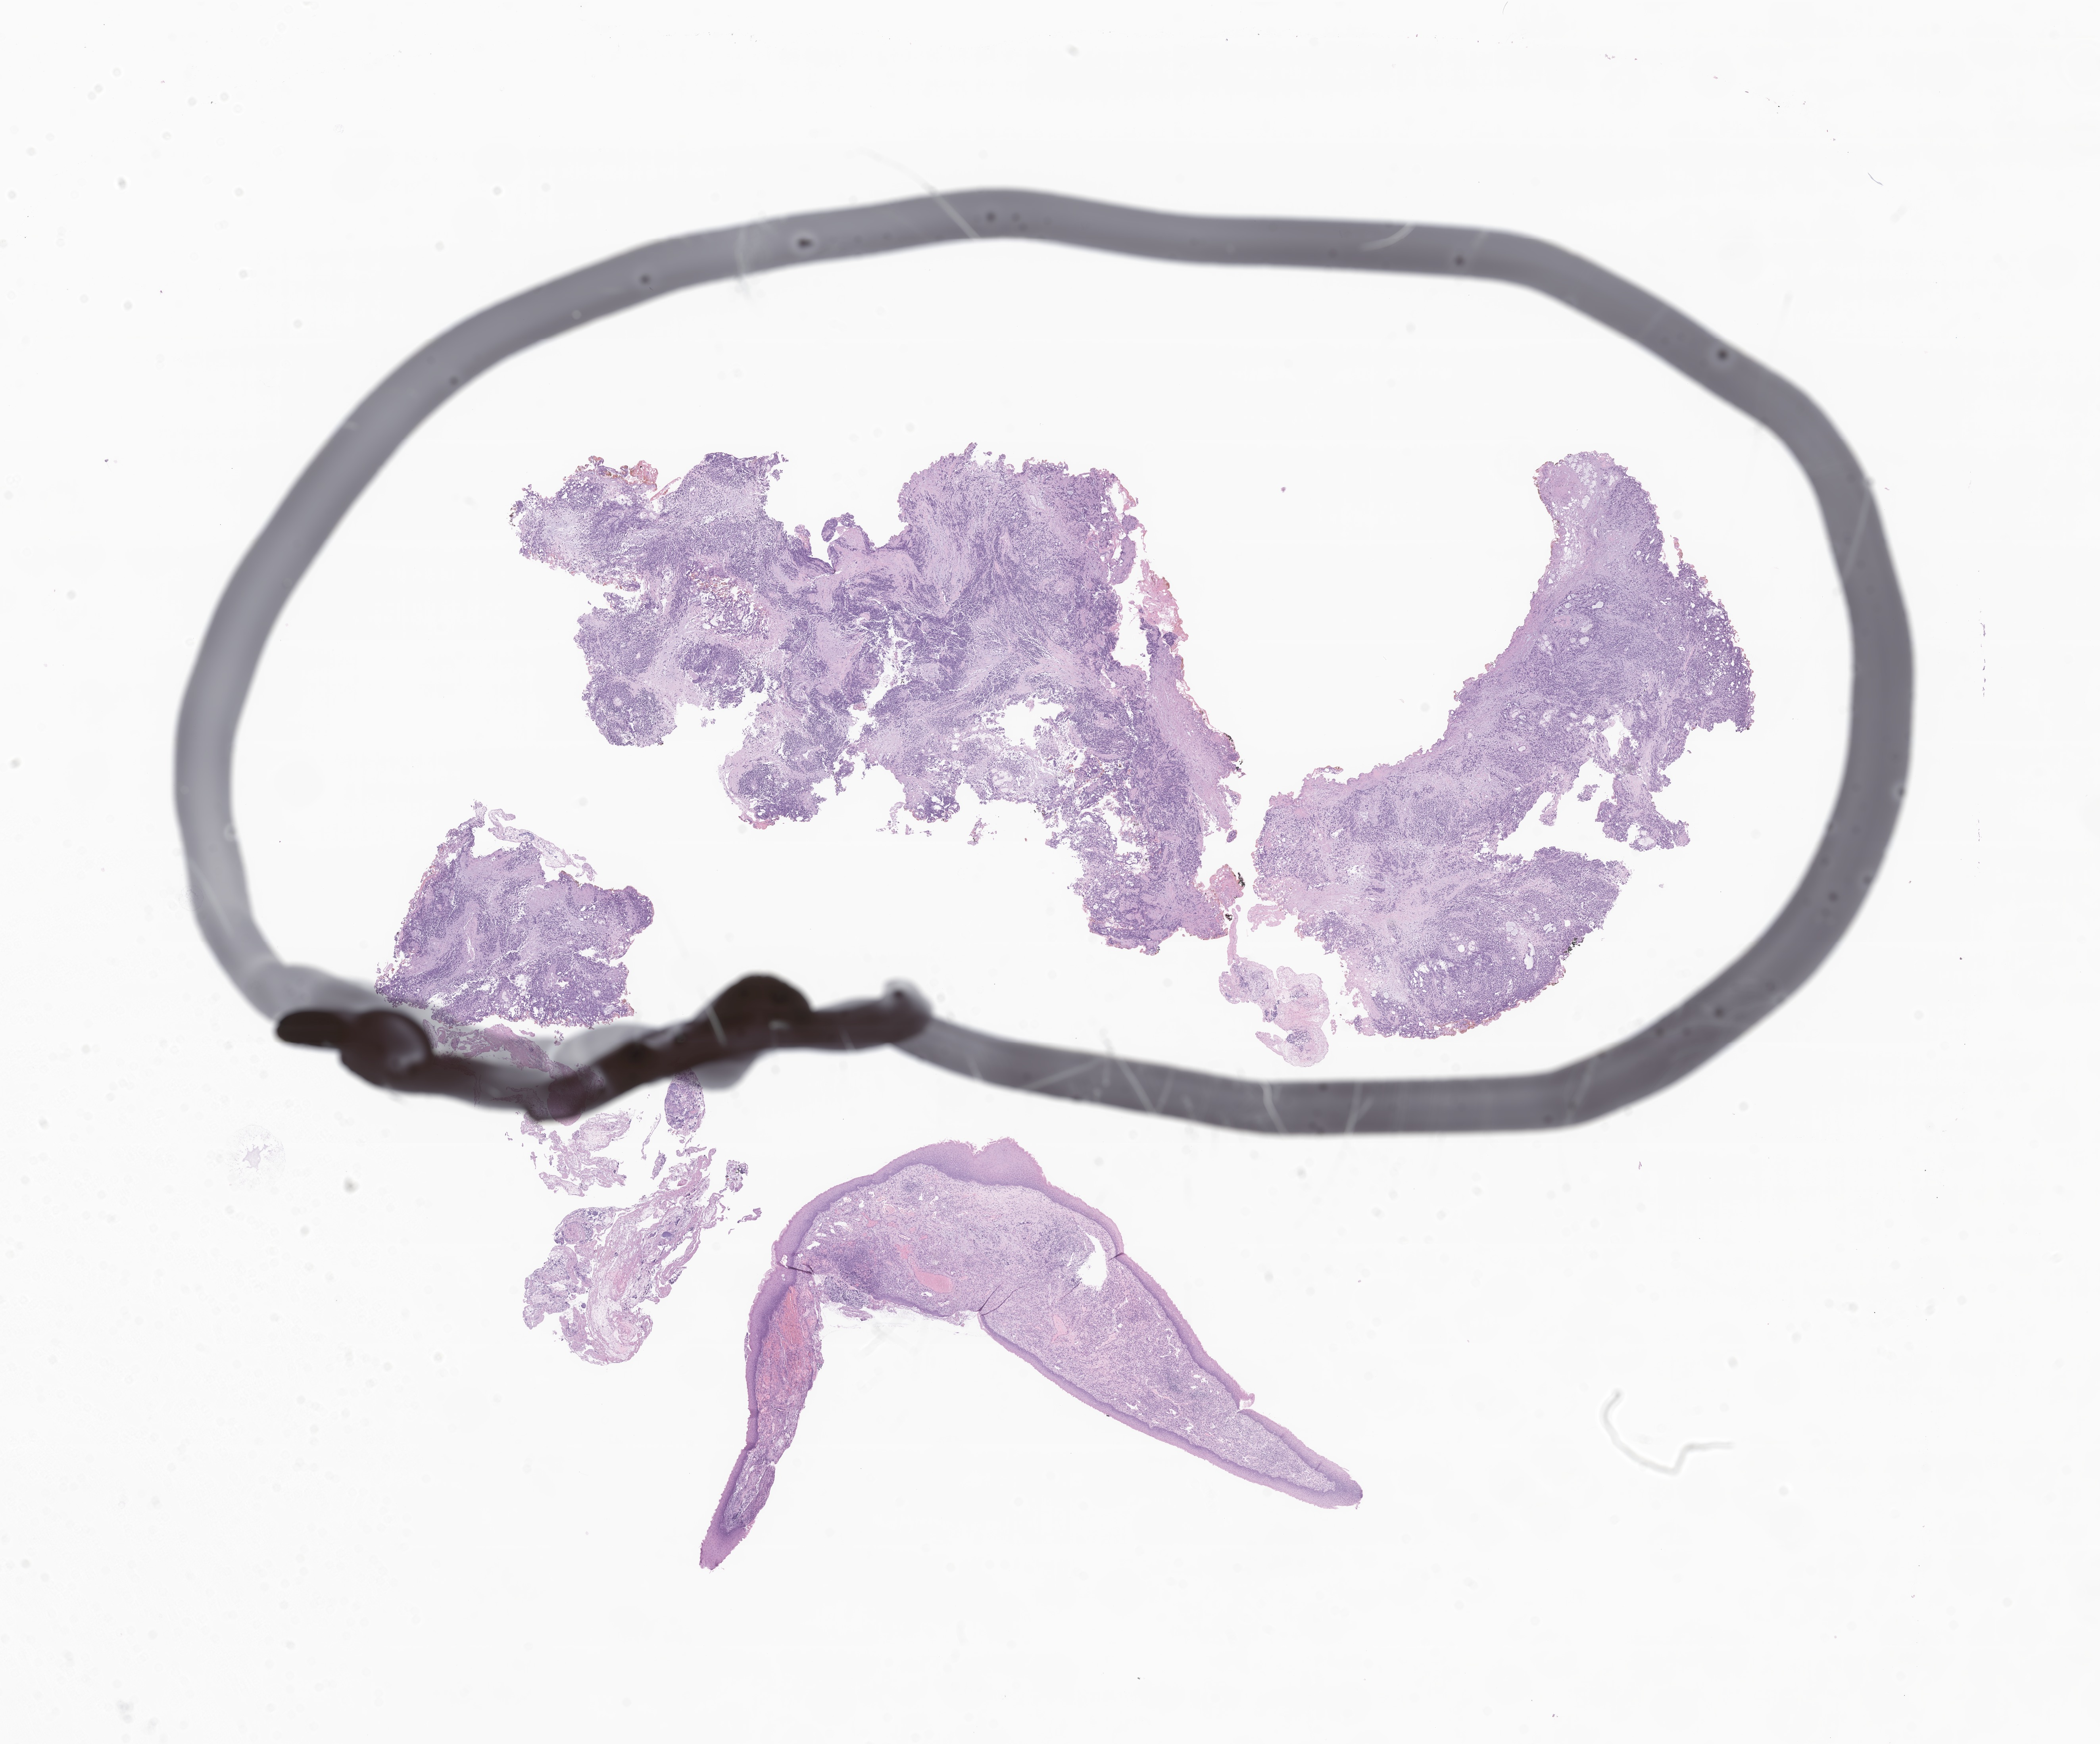
Digitized hematoxylin and eosin (H&E)-stained section of tumor tissue from the root of tongue — a low-resolution overview of the entire scanned area, about 22.3 x 18.5 mm; FFPE section. Female patient, age 53 months (4 years 5 months).
Diagnosis (ICD-O-3 morphology term): Rhabdomyosarcoma, NOS.